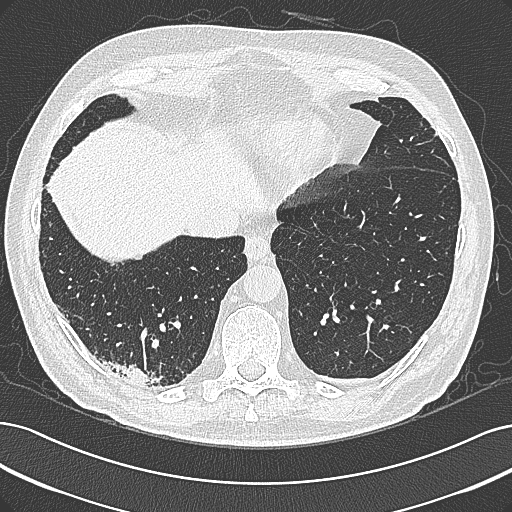
Low-dose screening chest CT, axial slice. Baseline screening round. Lung window (W 1500 / L -600 HU). 1 mm slice thickness. 120 kVp. Slice 227 of 355 in the series. 512 × 512 image matrix. Male participant, aged 68 years at enrolment. Former smoker at enrolment.
Lesion marked by an expert reader, bounding box <98,341,183,402> (left, top, right, bottom; pixels). Screening reader's record for this exam: no non-calcified nodule ≥4 mm recorded. Lung cancer was diagnosed 154 days after this screen: mucinous adenocarcinoma, right lower lobe, well differentiated (G1), stage IB (AJCC 6th edition), 50 mm at pathology.